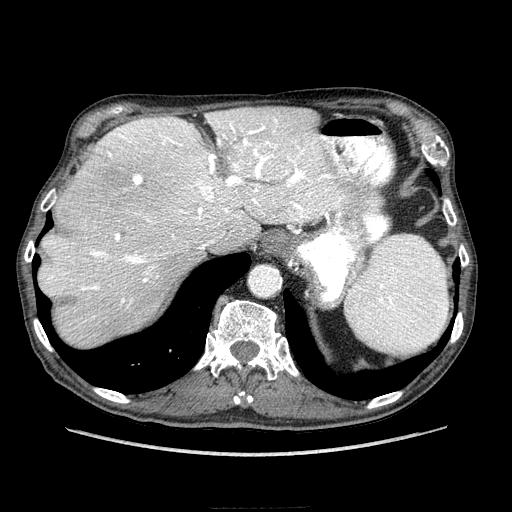
Contrast-enhanced abdominal CT (liver protocol), one axial slice; reconstruction kernel STANDARD; soft-tissue window (W 400 / L 40 HU); 2.5 mm slice thickness; 512 × 512 image matrix, field of view 380 × 380 mm. Case-level facts recorded for this patient, not image findings: diagnosis: hepatocellular carcinoma (patient treated with transarterial chemoembolisation; whether this scan precedes or follows treatment is not stated here); TNM stage (as recorded): Stage-IIIA; Child-Pugh class: A; tumour nodularity: multinodular; tumour size: 20 cm.
Structures marked on this image (semi-automatic segmentation, software-assisted and operator-edited):
- abdominal aorta: bounding box [x1, y1, x2, y2] px = [249, 266, 281, 296]
- liver parenchyma outside the tumour (the mass and vessels are separate outlines, so this box may not span the whole liver): [40, 108, 350, 346]
- liver vessels: [44, 114, 345, 318]